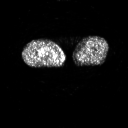
FDG PET of an extremity soft-tissue mass (from a PET/CT study), one axial slice. Position 231 of 311 along the scan axis. 128 × 128 image matrix, field of view 700 × 700 mm. Patient: male, 50 years. From the clinical record (not read from this slice): histological type: undifferentiated - pleiomorphic; grade: high; site of the primary tumour: right thigh.
Annotated regions visible in this slice (expert contour drawn on MRI and transferred to this co-registered scan by the dataset authors):
- gross tumour volume including surrounding oedema: bounding box (x1, y1, x2, y2) in pixels: (44, 53, 47, 57)